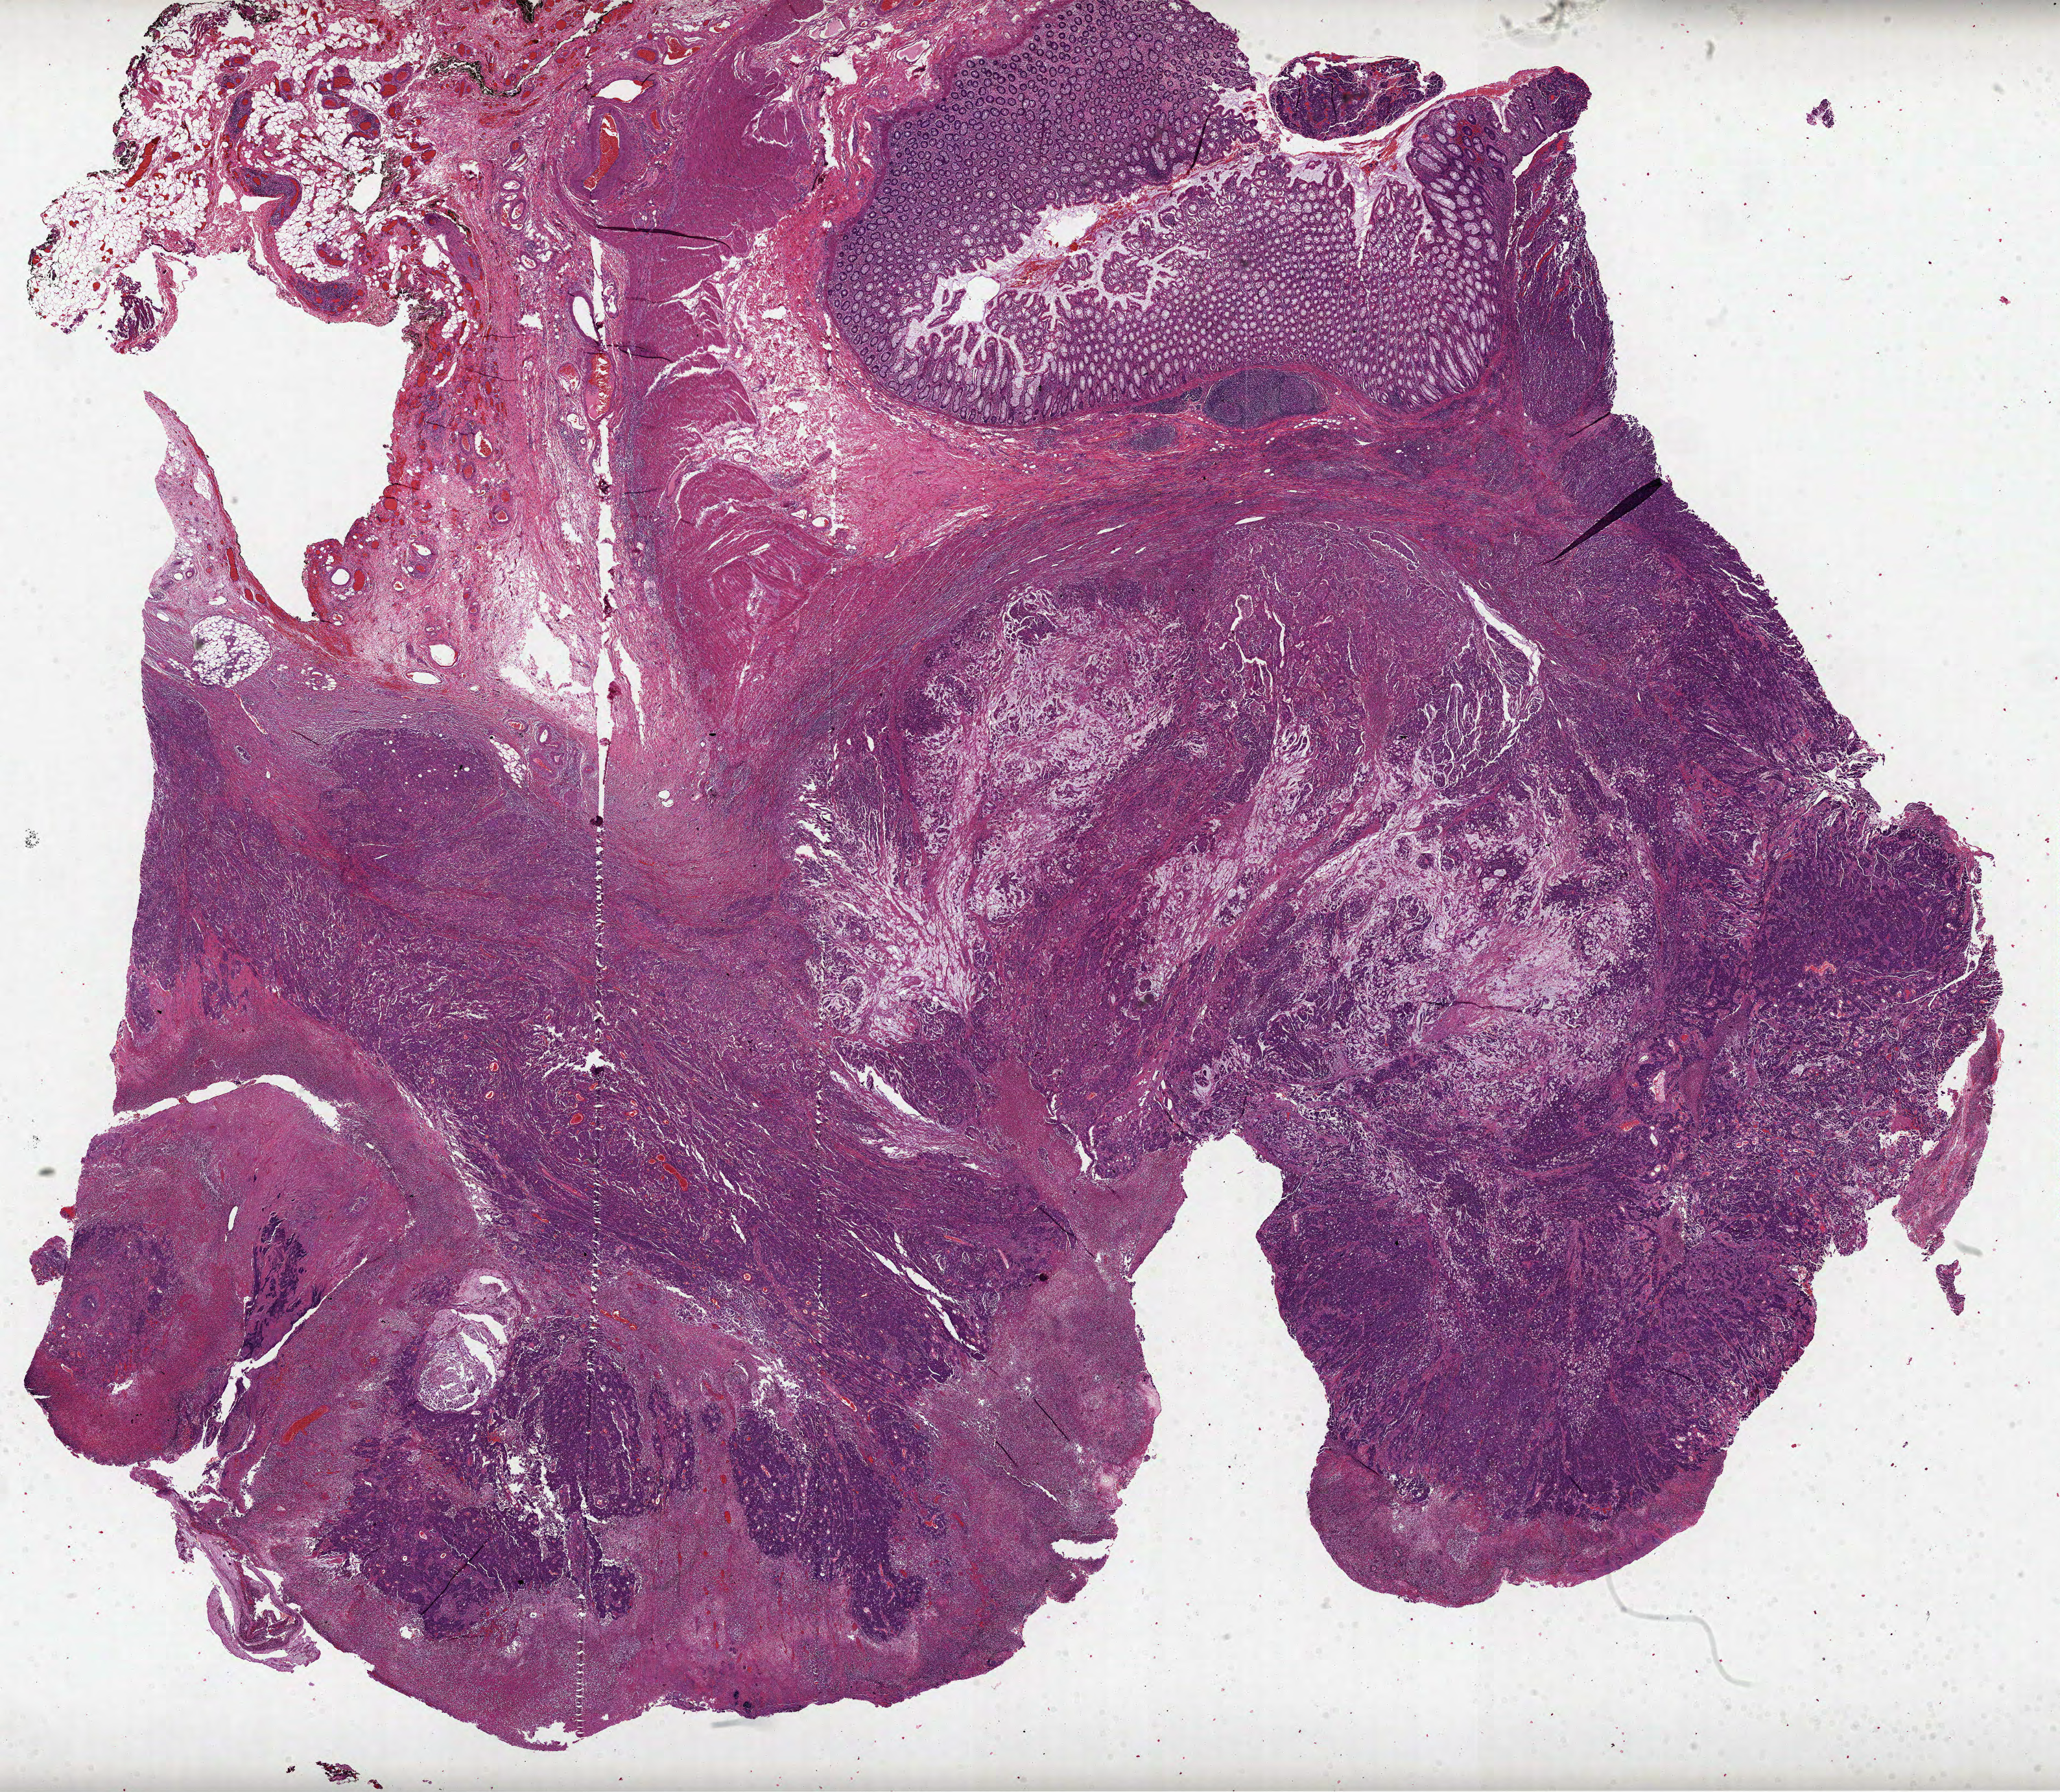
H&E whole-slide image — low-resolution overview of the scanned area, about 25.6 x 22.3 mm (acquisition: 40x scan). Formalin-fixed paraffin-embedded (FFPE) diagnostic section. Primary tumour sample from the colon. Male, age 69 years at initial diagnosis.
Histologic diagnosis: Adenocarcinoma, NOS (ascending colon).